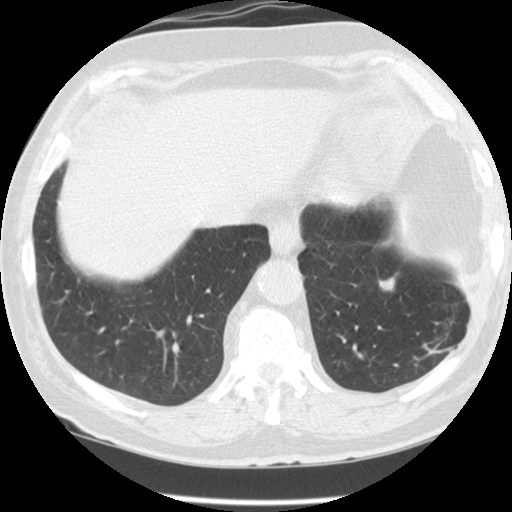
Low-dose screening chest CT, one axial slice; position 33 of 127 along the scan axis; reconstruction kernel STANDARD; lung window (W 1500 / L -600 HU); 2.5 mm slice thickness; 512 × 512 image matrix, field of view 340 × 340 mm.
Annotated regions visible in this slice (outlined manually by an expert reader):
- lesion 1 (tumor, lower lobe of left lung): bounding box (x1, y1, x2, y2) in pixels: (379, 278, 394, 290)